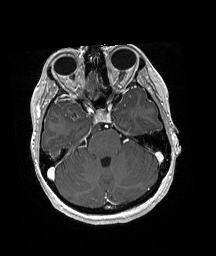
Brain MRI from a brain-tumour surgery series, one axial slice. Position 128 of 192 along the scan axis. T1-weighted post-contrast. 216 × 256 image matrix. Case-level facts recorded for this patient, not image findings: histopathology: Oligodendroglioma; WHO grade: 3; IDH mutation: yes.
Structures marked on this image (outlined manually by an expert reader):
- tumour: bounding box (x1, y1, x2, y2) in pixels: (88, 77, 95, 92)